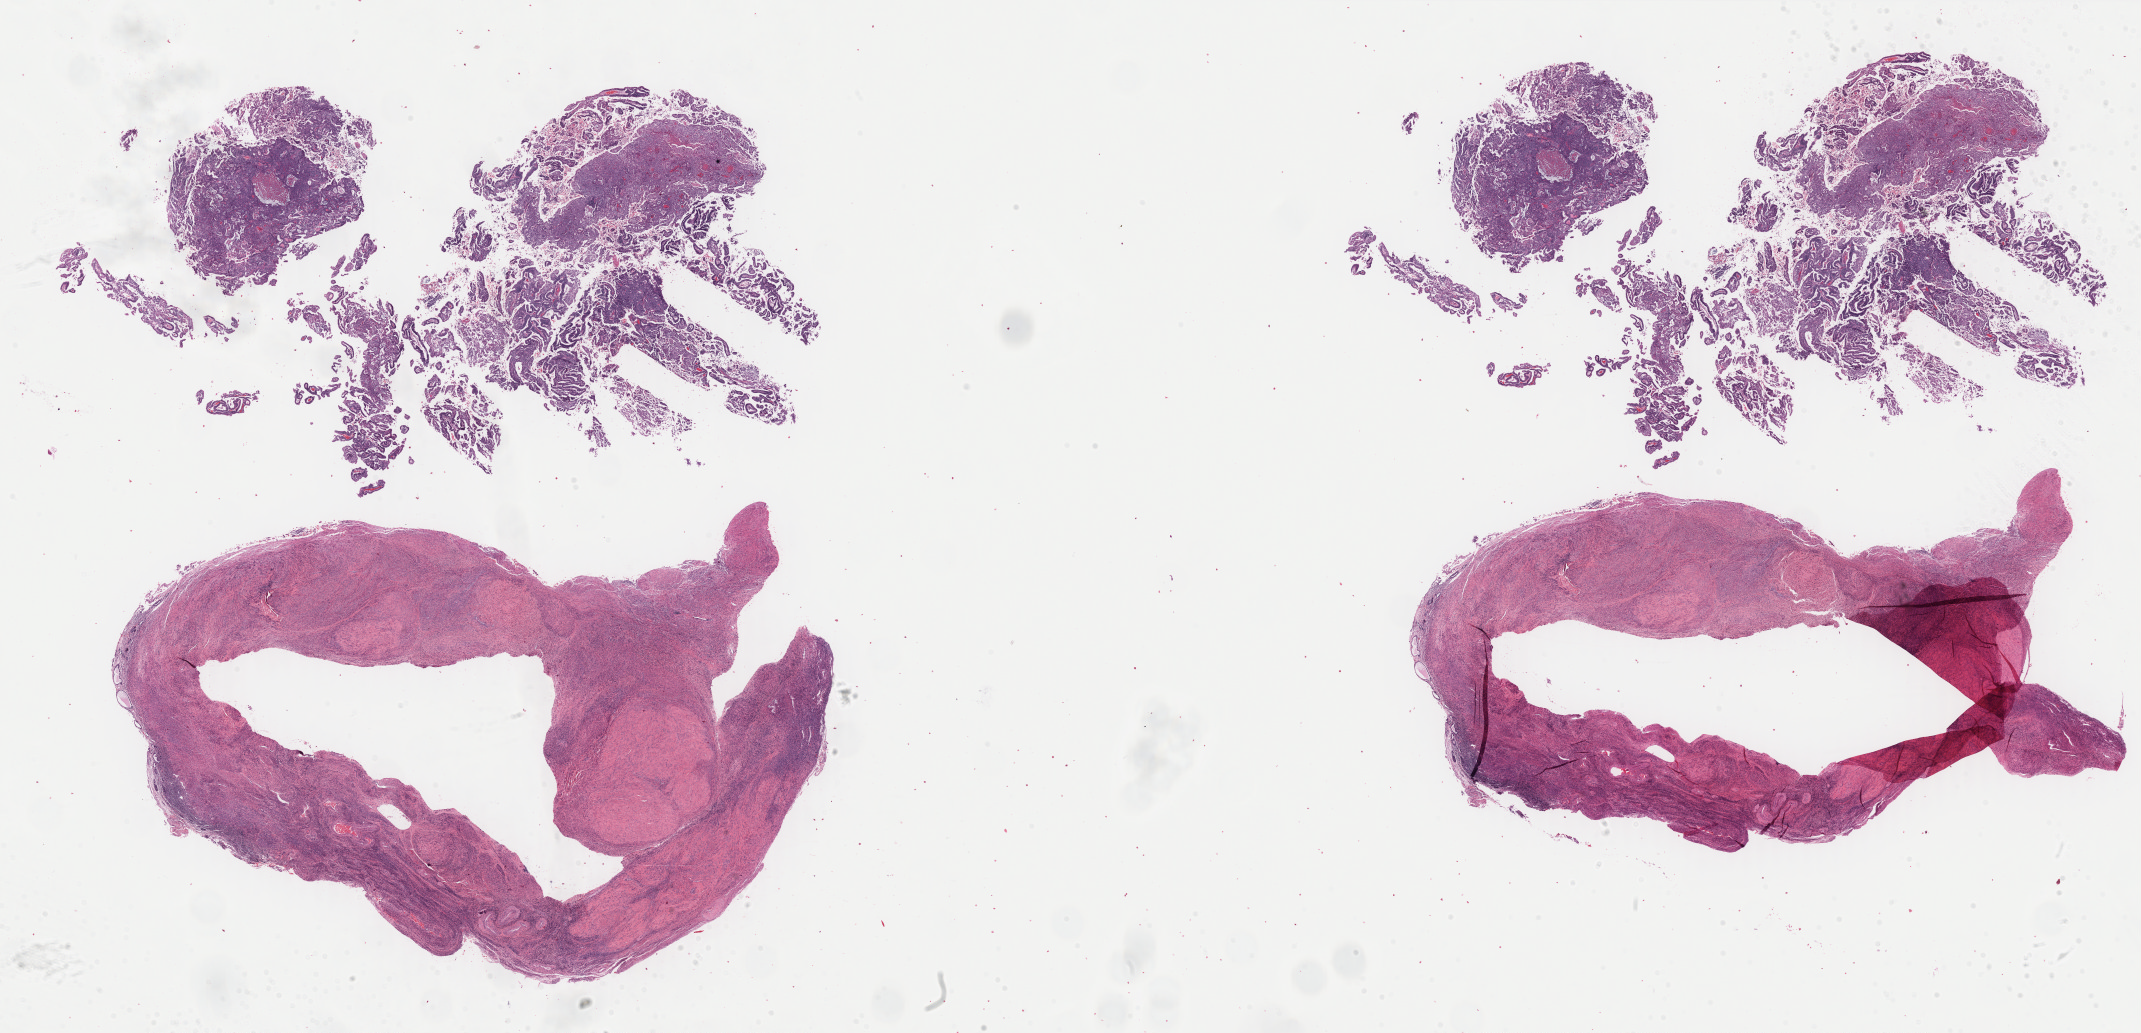
H&E whole-slide image, shown as a low-resolution overview of the whole scanned area (about 33.9 x 16.4 mm, slide scanned at 40x). Formalin-fixed paraffin-embedded (FFPE) diagnostic section. Uterus, primary tumour sample. Female, age 56 years at initial diagnosis. Histologic grade: G3 (poorly differentiated).
Diagnosis: Serous cystadenocarcinoma, NOS (endometrium). FIGO stage: IB.